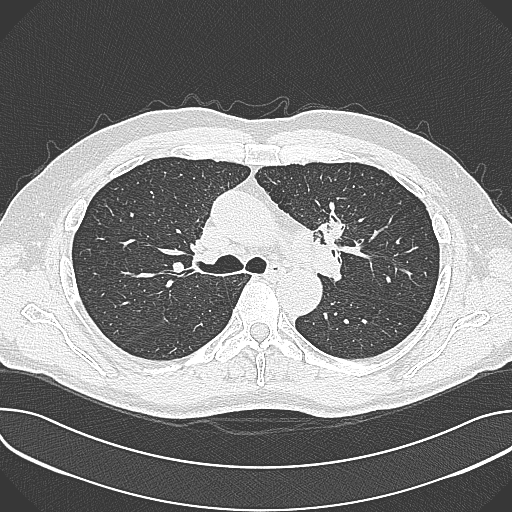
Low-dose screening chest CT, axial slice, first (baseline) screen, lung window (W 1500 / L -600 HU), 1 mm slice thickness, slice 114 of 361 in the series, 512 × 512 image matrix, field of view 380 × 380 mm. Male, age 59 years at enrolment. Current smoker at enrolment.
Expert reader's lesion annotation, box from (x=303, y=193) to (x=365, y=256) px. The screening reader recorded 2 non-calcified nodules or masses ≥4 mm on this exam (left upper lobe, left upper lobe); which of them this box marks is not recorded. Official screen result: positive, change unspecified: nodule(s) >= 4 mm or enlarging nodule(s), mass(es), or other non-specific abnormalities suspicious for lung cancer. Later outcome: lung cancer diagnosed 21 days after this screen — non-small cell carcinoma, left upper lobe, poorly differentiated (G3), stage IIIA (AJCC 6th edition), 35 mm at pathology.